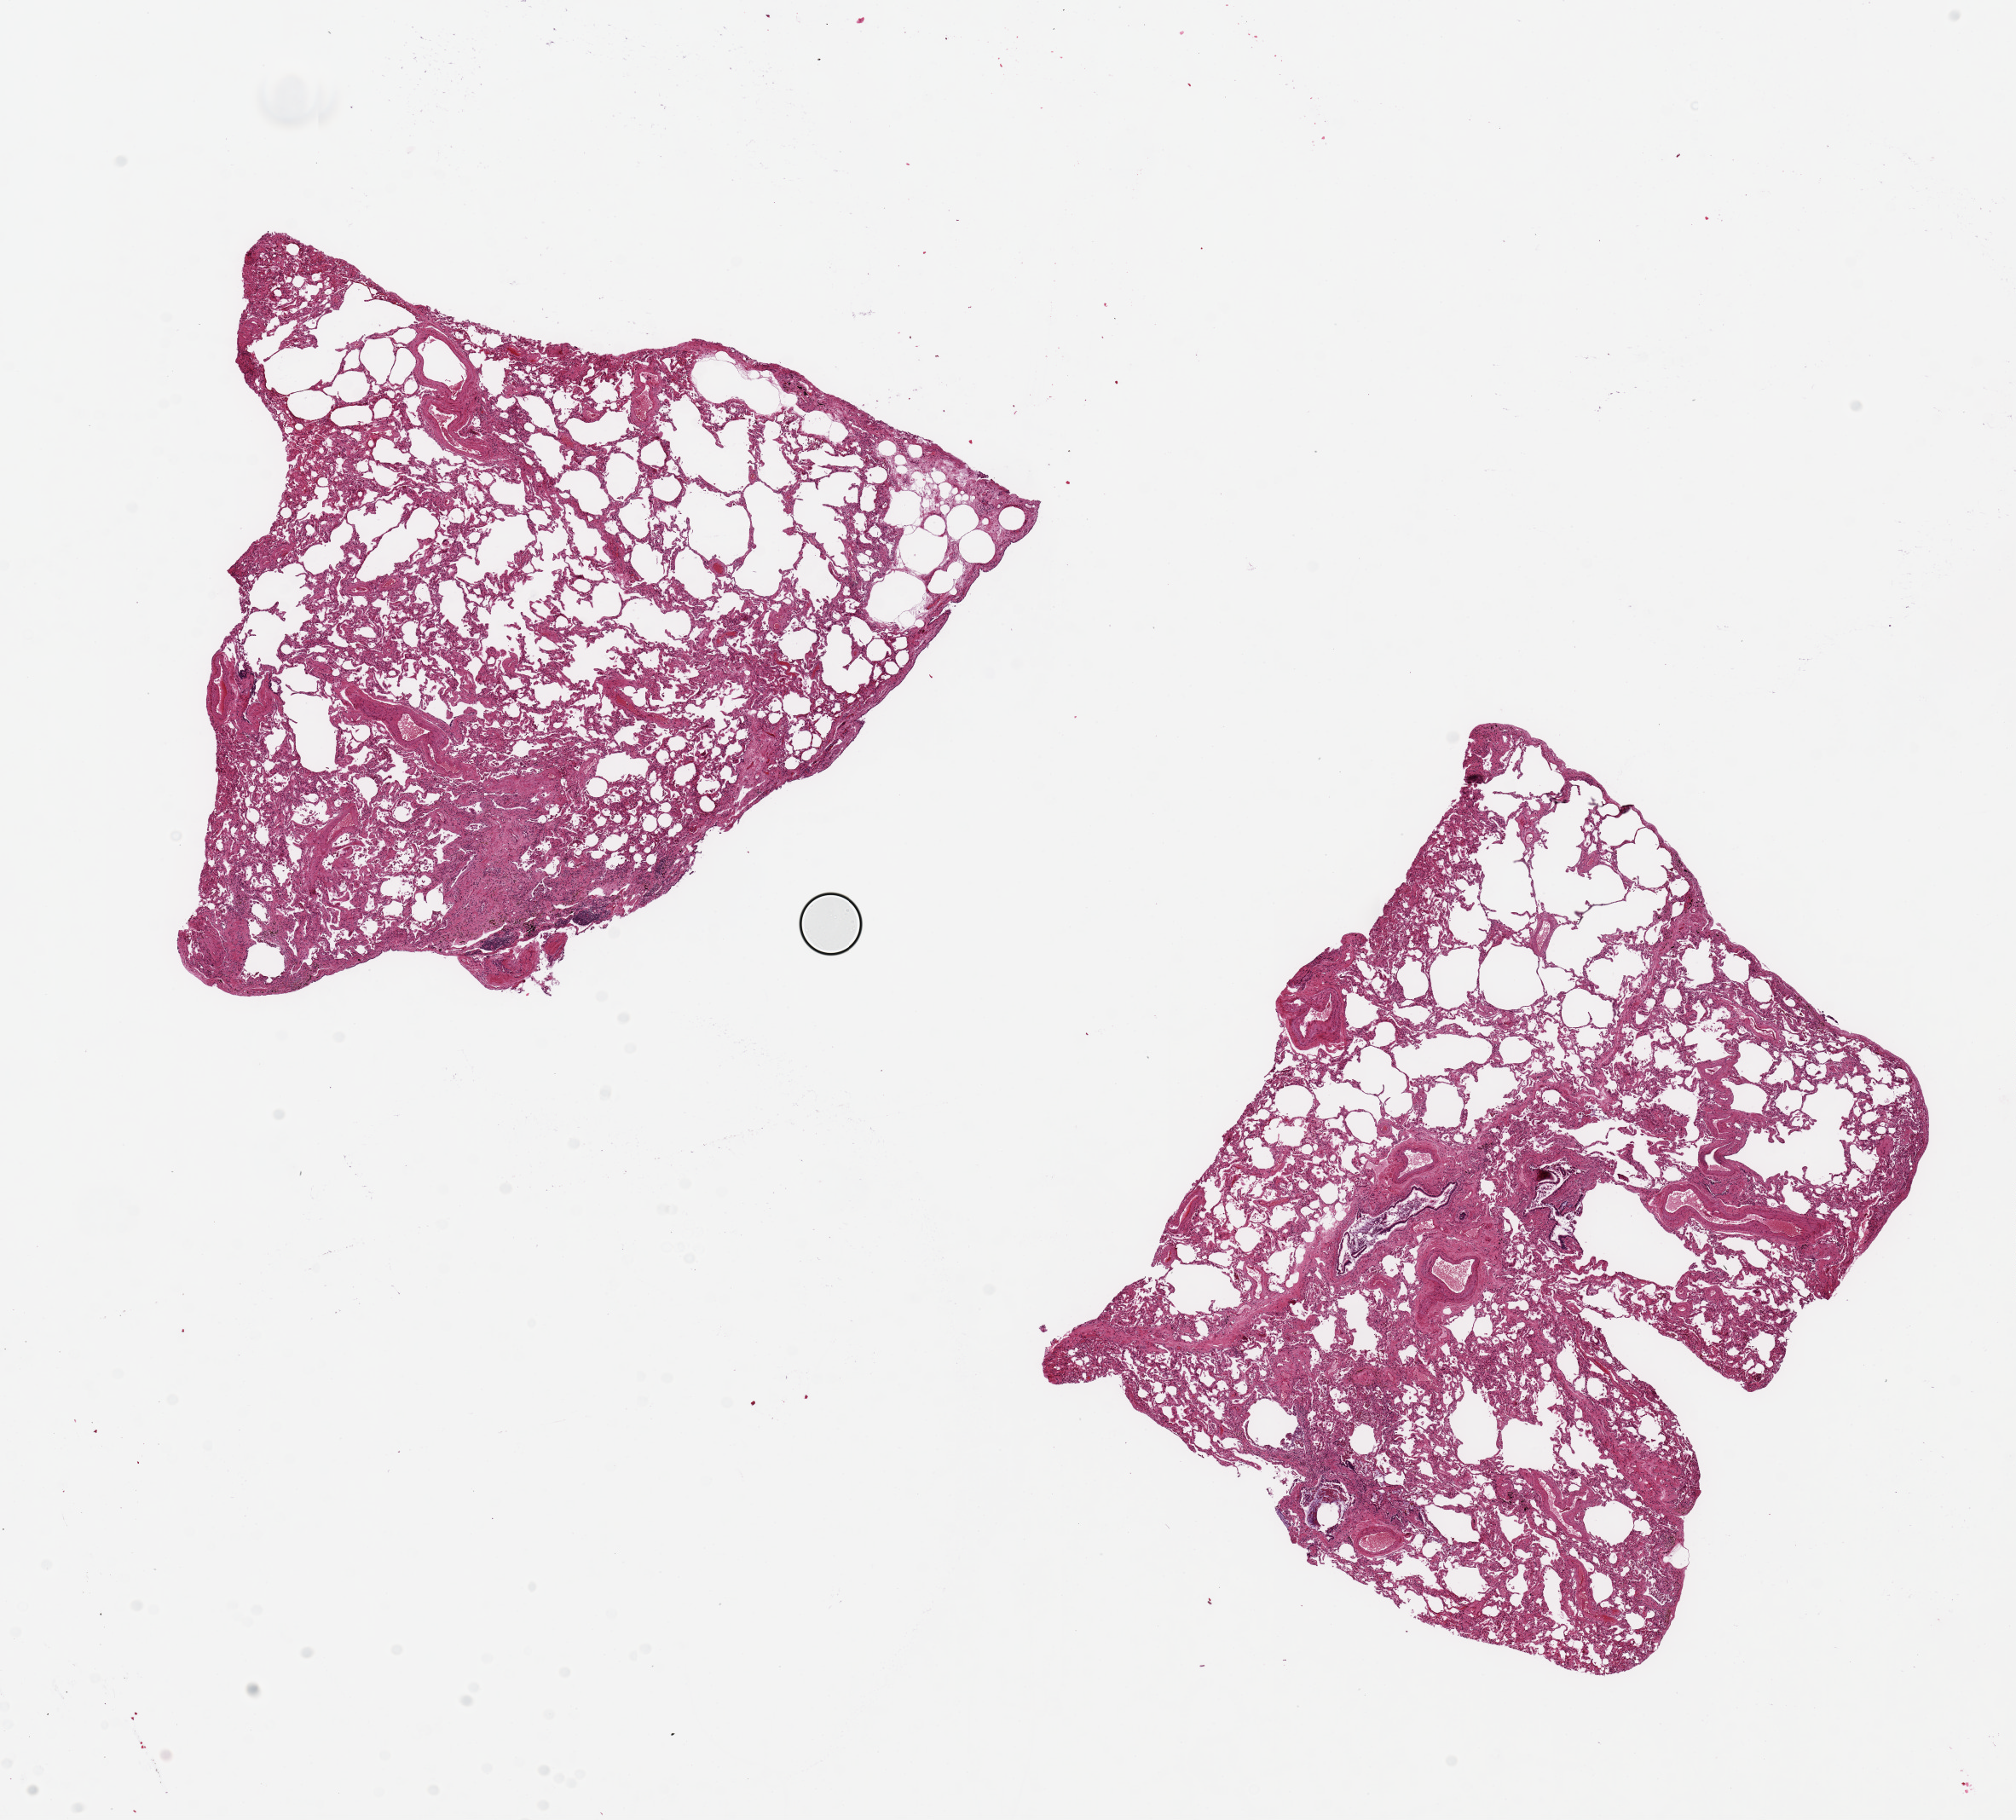
Hematoxylin and eosin (H&E) whole-slide image — low-resolution overview of the scanned area, about 18.7 x 16.9 mm, PAXgene-fixed, paraffin-embedded tissue, target tissue: lung, tissue donor sample.
Reviewer comment on this tissue sample: 2 pieces, 7x6 & 7.5x7mm; heart failure cells, focal fibrosis.